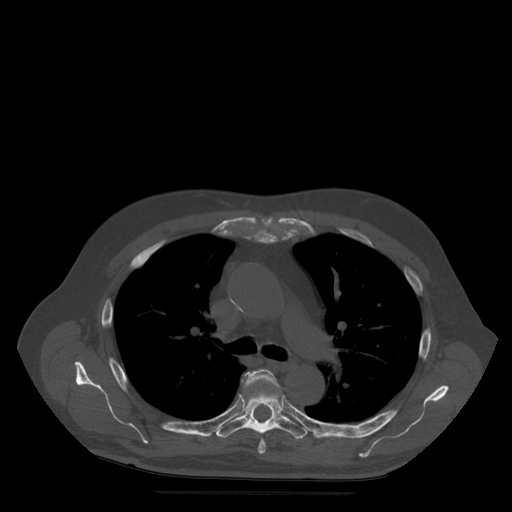
CT including the spine, one axial slice. Position 360 of 522 along the scan axis. Bone window (W 1800 / L 400 HU). 1.25 mm slice thickness. 512 × 512 image matrix. Patient age 72 years. From the clinical record (not read from this slice): primary cancer: prostate.
Annotated regions visible in this slice (semi-automatically segmented with operator editing):
- T5 vertebra: bounding box <245,369,281,454> (left, top, right, bottom; pixels)
- T6 vertebra: <217,372,308,440>